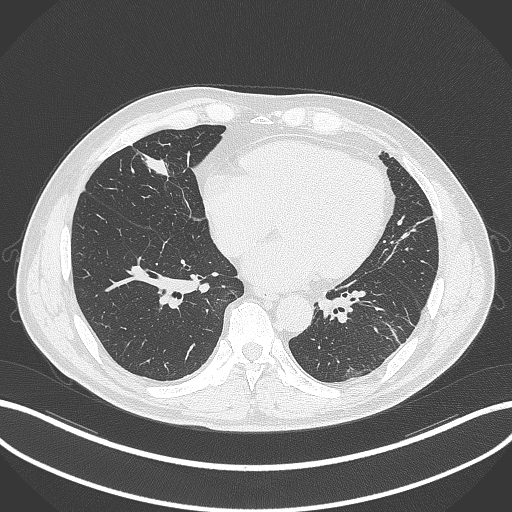
Chest CT, one axial slice; slice 98 of 399 in the series (ordered by position); 120 kVp; lung window (W 1500 / L -600 HU); 1 mm slice thickness; 512 × 512 image matrix, field of view 400 × 400 mm. Male patient, age 59 years. From the clinical record (not read from this slice): clinical TNM (as recorded): T2a N1 M0.
Annotated regions visible in this slice (bounding box drawn by a radiologist):
- lung tumour (recorded histology: adenocarcinoma): box from (x=136, y=148) to (x=174, y=186) px